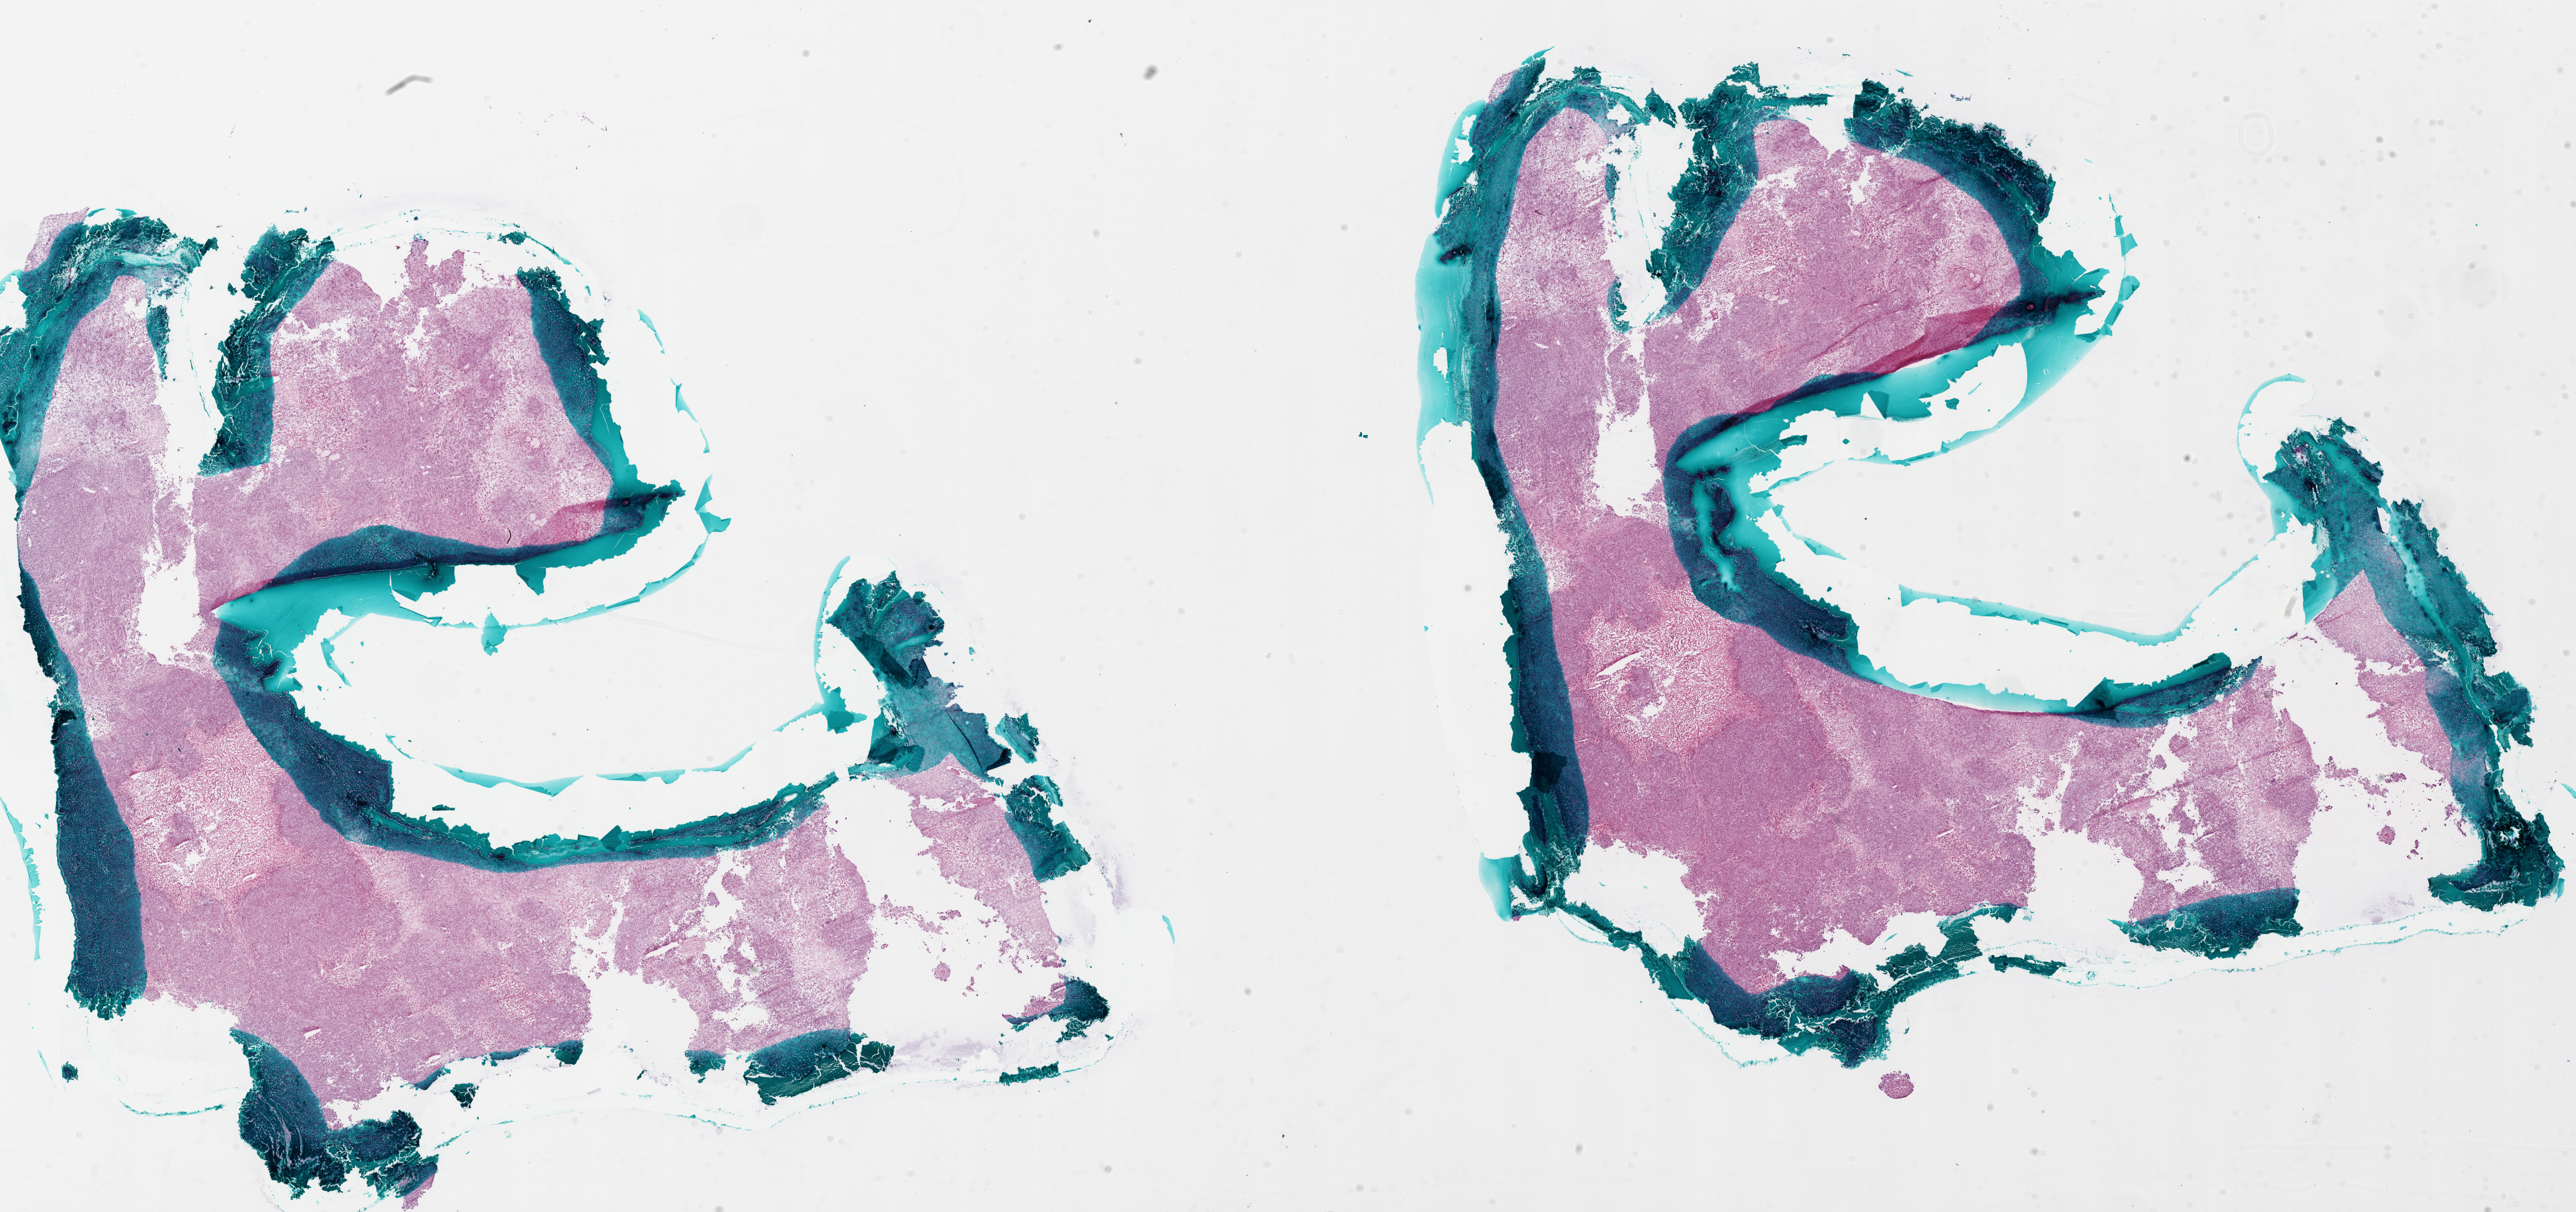
Whole-slide histology image, Hematoxylin and eosin (H&E) stained, a low-resolution overview of the entire scanned area, about 35.0 x 16.4 mm, frozen section, sample: primary tumour, brain. Patient: male, age at initial diagnosis 43 years. Composition of this section per pathologist review: tumour cells 80%, tumour nuclei 100%, normal cells 0%, stromal cells 0%, necrosis 20%.
* pathologic diagnosis: Glioblastoma